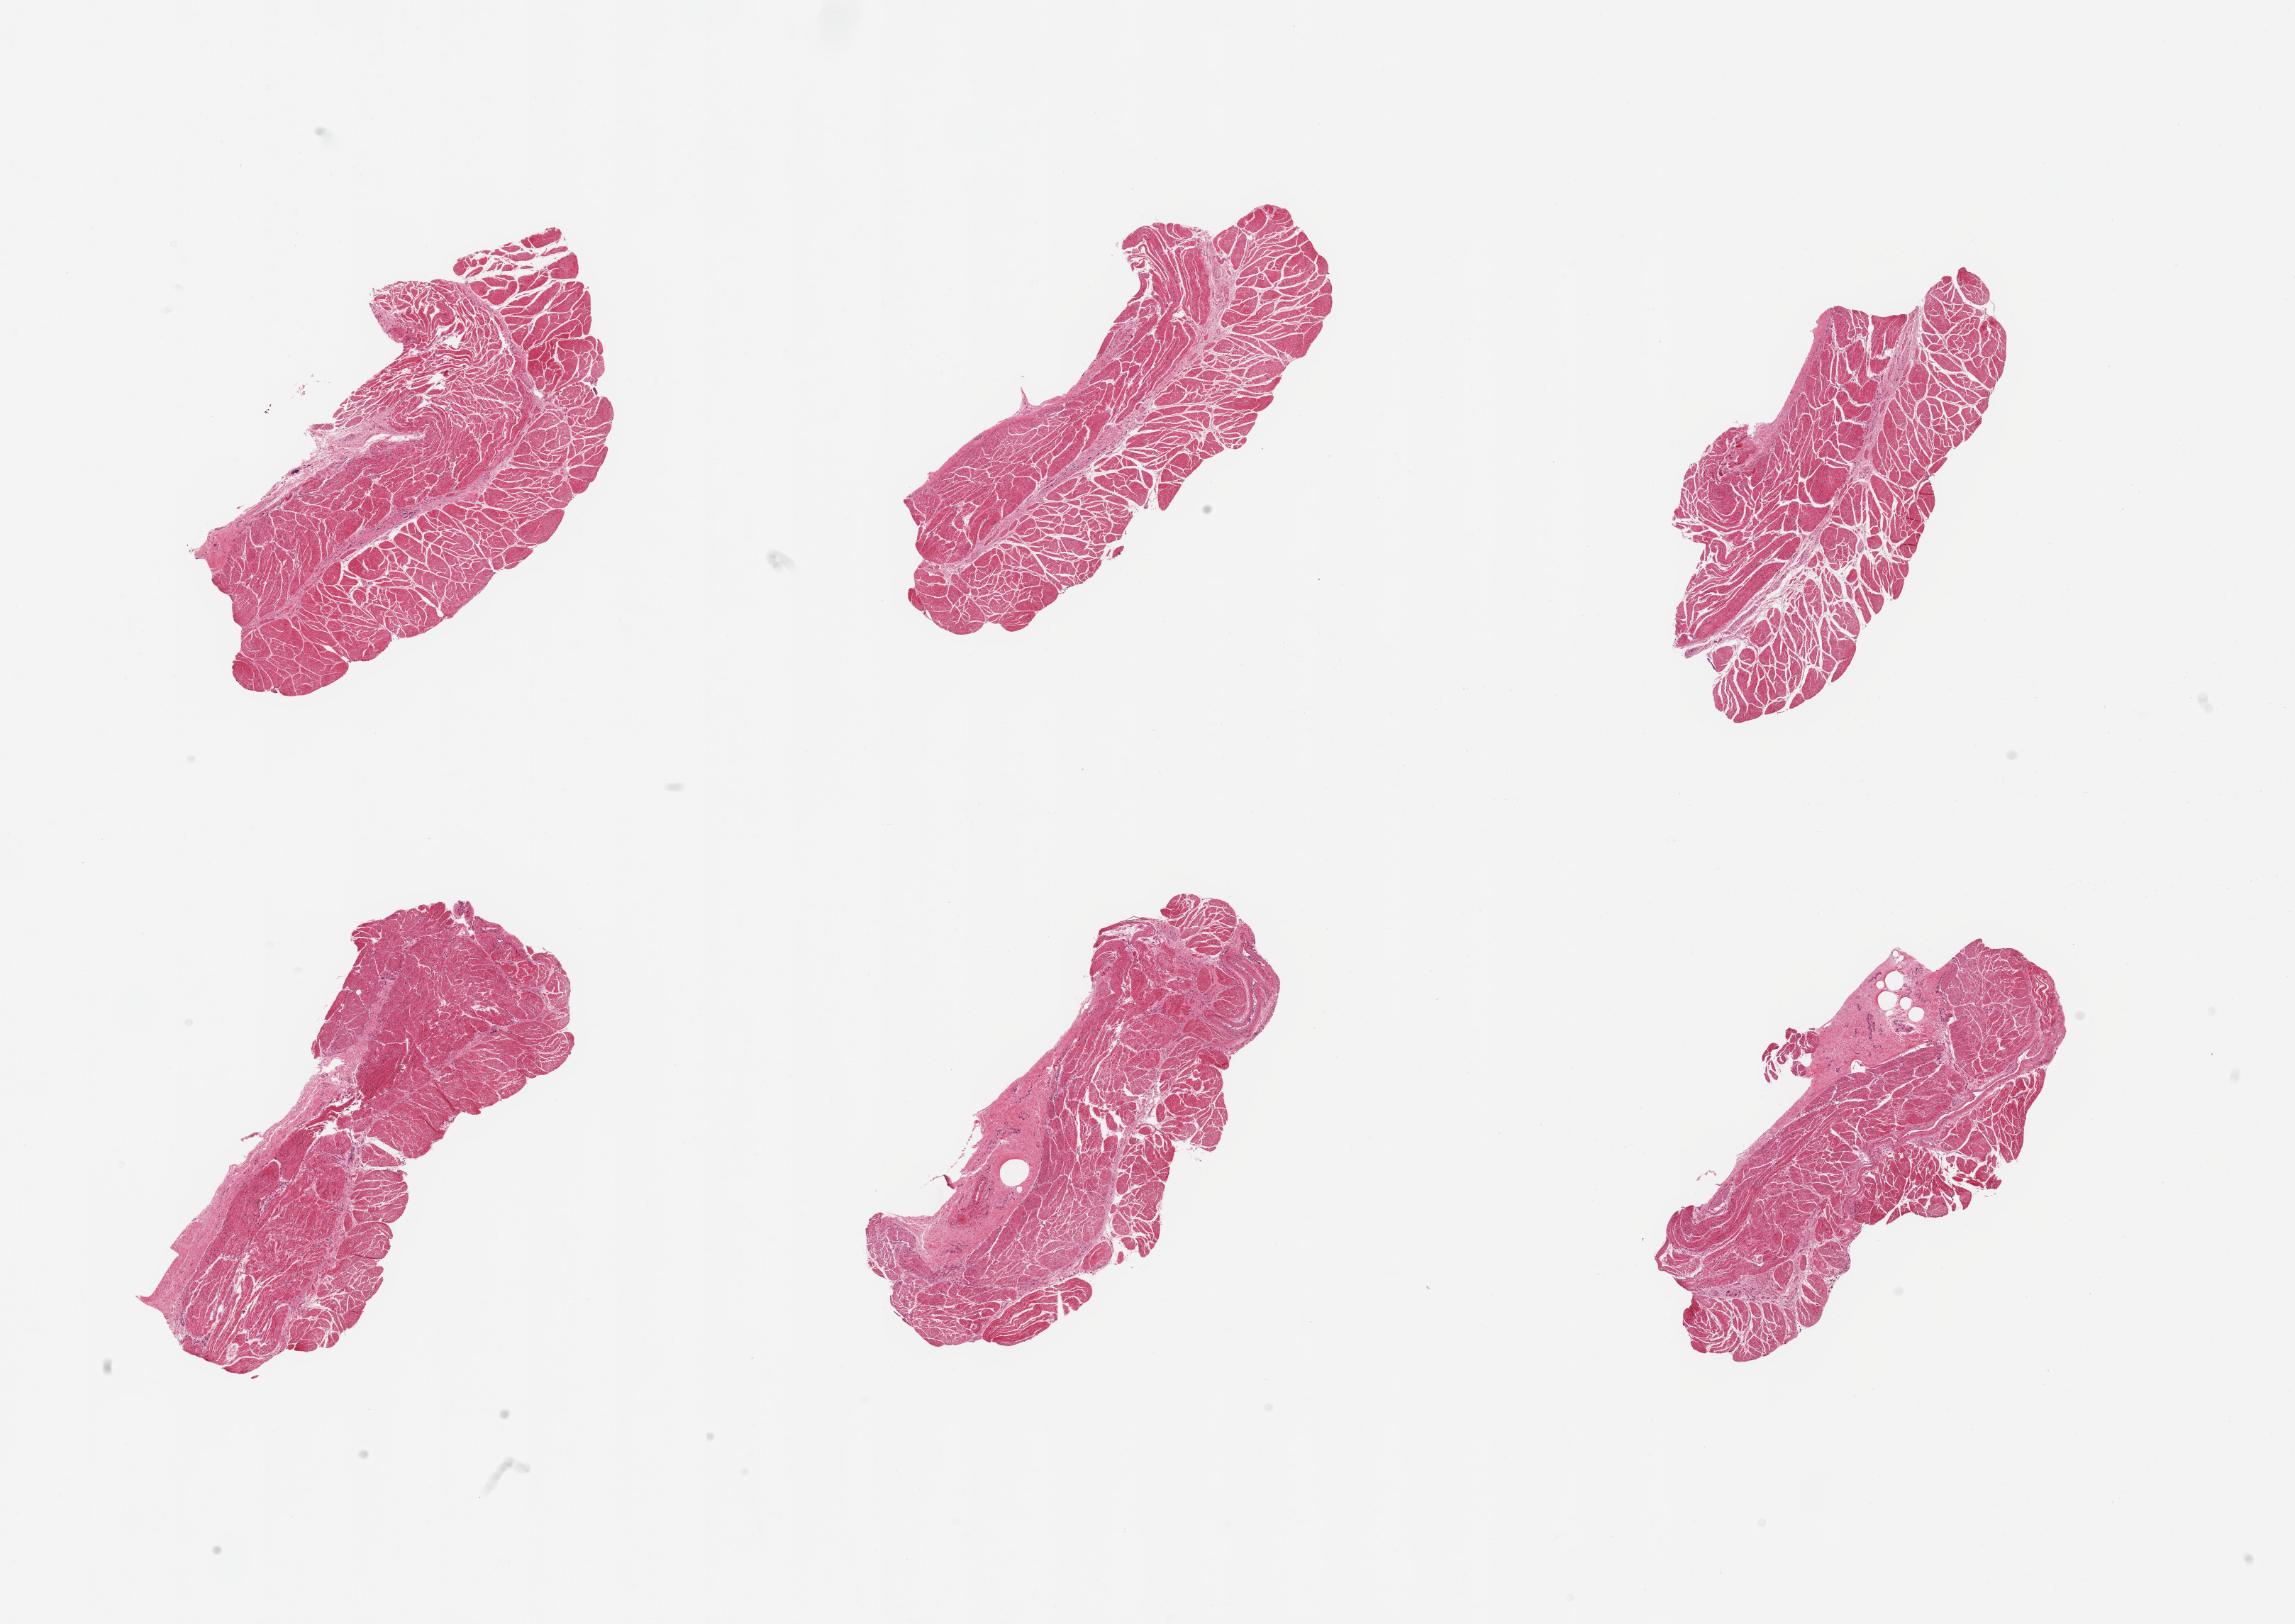
Digitized haematoxylin and eosin-stained section, brightfield — shown as a low-resolution overview of the whole scanned area (about 25.6 x 18.1 mm); PAXgene-fixed paraffin-embedded (PFPE) section; sampled site (target tissue): esophageal muscle; donor tissue sample. Male donor.
- reviewer comment on this tissue sample: 6 pieces; target muscularis